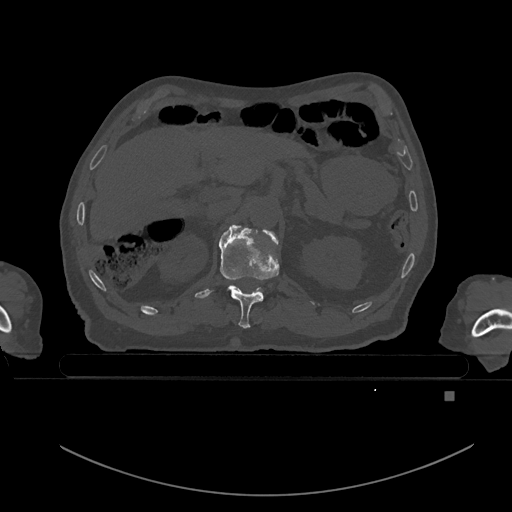
CT including the spine, one axial slice. Position 10 of 969 along the scan axis. Bone window (W 1800 / L 400 HU). 0.5 mm slice thickness. 512 × 512 image matrix, field of view 456 × 456 mm. Male patient, age 82 years. From the clinical record (not read from this slice): primary cancer: prostate; vertebrae with lytic lesions (as recorded): T11, T9, T8, T2.
Outlined on this slice (semi-automatically segmented with operator editing):
- T11 vertebra: bounding box [x1, y1, x2, y2] px = [218, 227, 280, 328]